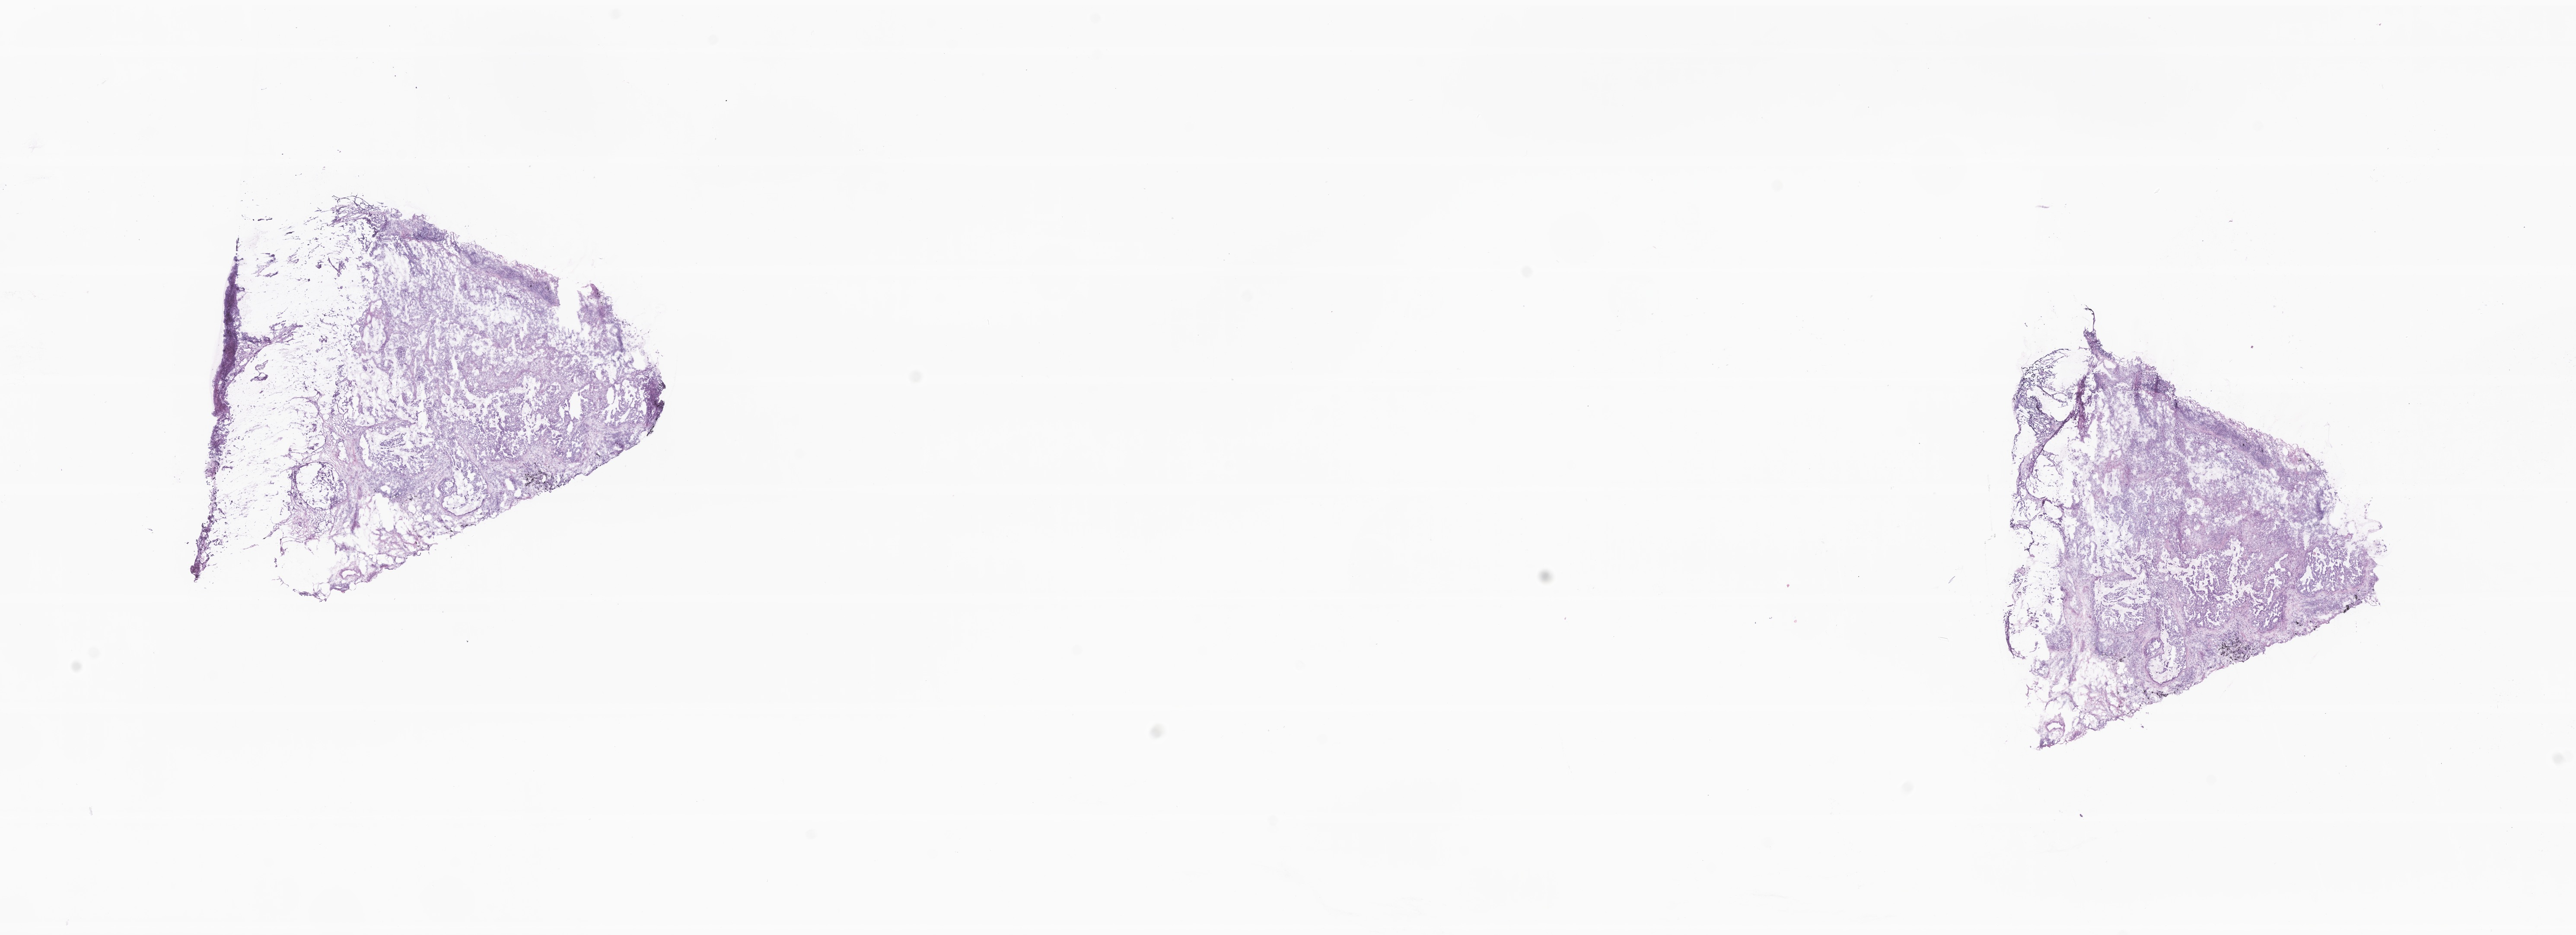
Haematoxylin and eosin whole-slide image — a low-resolution overview of the entire scanned area, about 25.1 x 9.1 mm, frozen section (tissue freezing medium), metastatic tumor tissue. Patient: male, age at initial diagnosis 72 years. Composition of this section per pathologist review: tumor cells 27%, tumor nuclei 70%, stromal cells 58%, necrosis 1%, normal cells 14%. Inflammatory infiltration, as recorded: lymphocyte infiltration 13%, monocyte infiltration 2%, neutrophil infiltration 0%.
Patient diagnosis (primary): Mucinous adenocarcinoma. Section: top of the tissue portion.